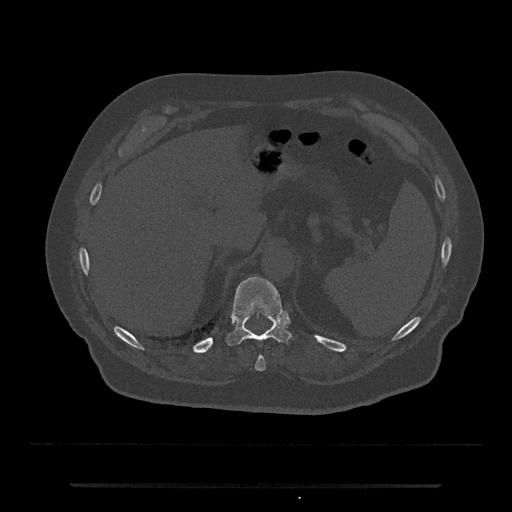
CT including the spine, one axial slice. Position 657 of 797 along the scan axis. Bone window (W 1800 / L 400 HU). 512 × 512 image matrix. Patient: male, 80 years. Case-level facts recorded for this patient, not image findings: primary cancer: prostate; vertebrae with lytic lesions (as recorded): L1, T11.
Structures marked on this image (semi-automatically segmented with operator editing):
- T10 vertebra: box from (x=255, y=356) to (x=266, y=371) px
- T11 vertebra: (x=226, y=276)–(x=292, y=345)